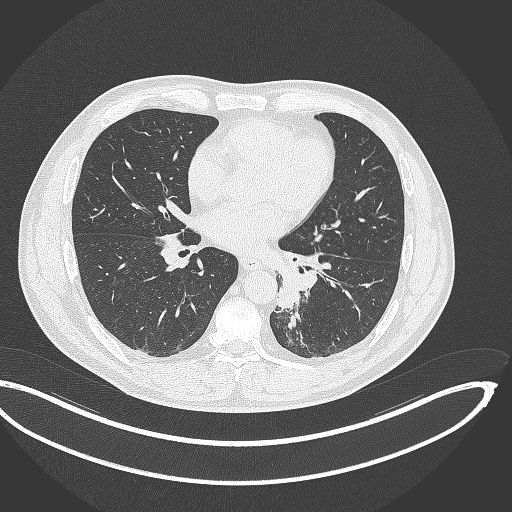
Chest CT, one axial slice; position 163 of 362 along the scan axis; 120 kVp; lung window (W 1500 / L -600 HU); 1 mm slice thickness; 512 × 512 image matrix. Male patient, age 50 years. Case-level facts recorded for this patient, not image findings: clinical TNM (as recorded): T2a N3 M0.
Outlined on this slice (rectangle marked by the reading radiologist):
- lung tumour (recorded histology: squamous cell carcinoma): box from (x=276, y=276) to (x=303, y=311) px